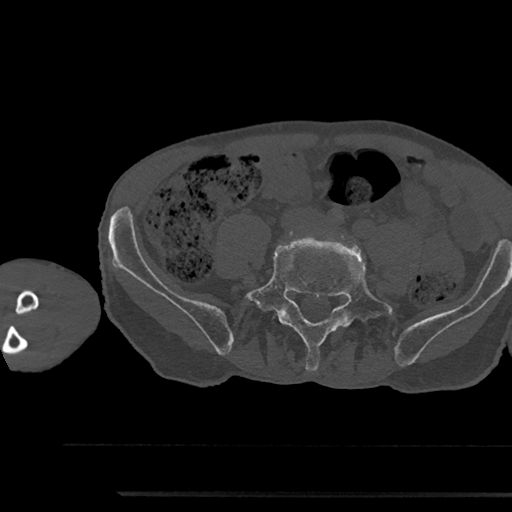
CT including the spine, one axial slice. Slice 353 of 797 in the series (ordered by position). Reconstruction kernel Br40s/3. 120 kVp. Bone window (W 1800 / L 400 HU). 512 × 512 image matrix, field of view 367 × 367 mm. Male patient, age 79 years. From the clinical record (not read from this slice): primary cancer: prostate.
Structures marked on this image (semi-automatically segmented with operator editing):
- L5 vertebra: box from (x=242, y=238) to (x=396, y=371) px